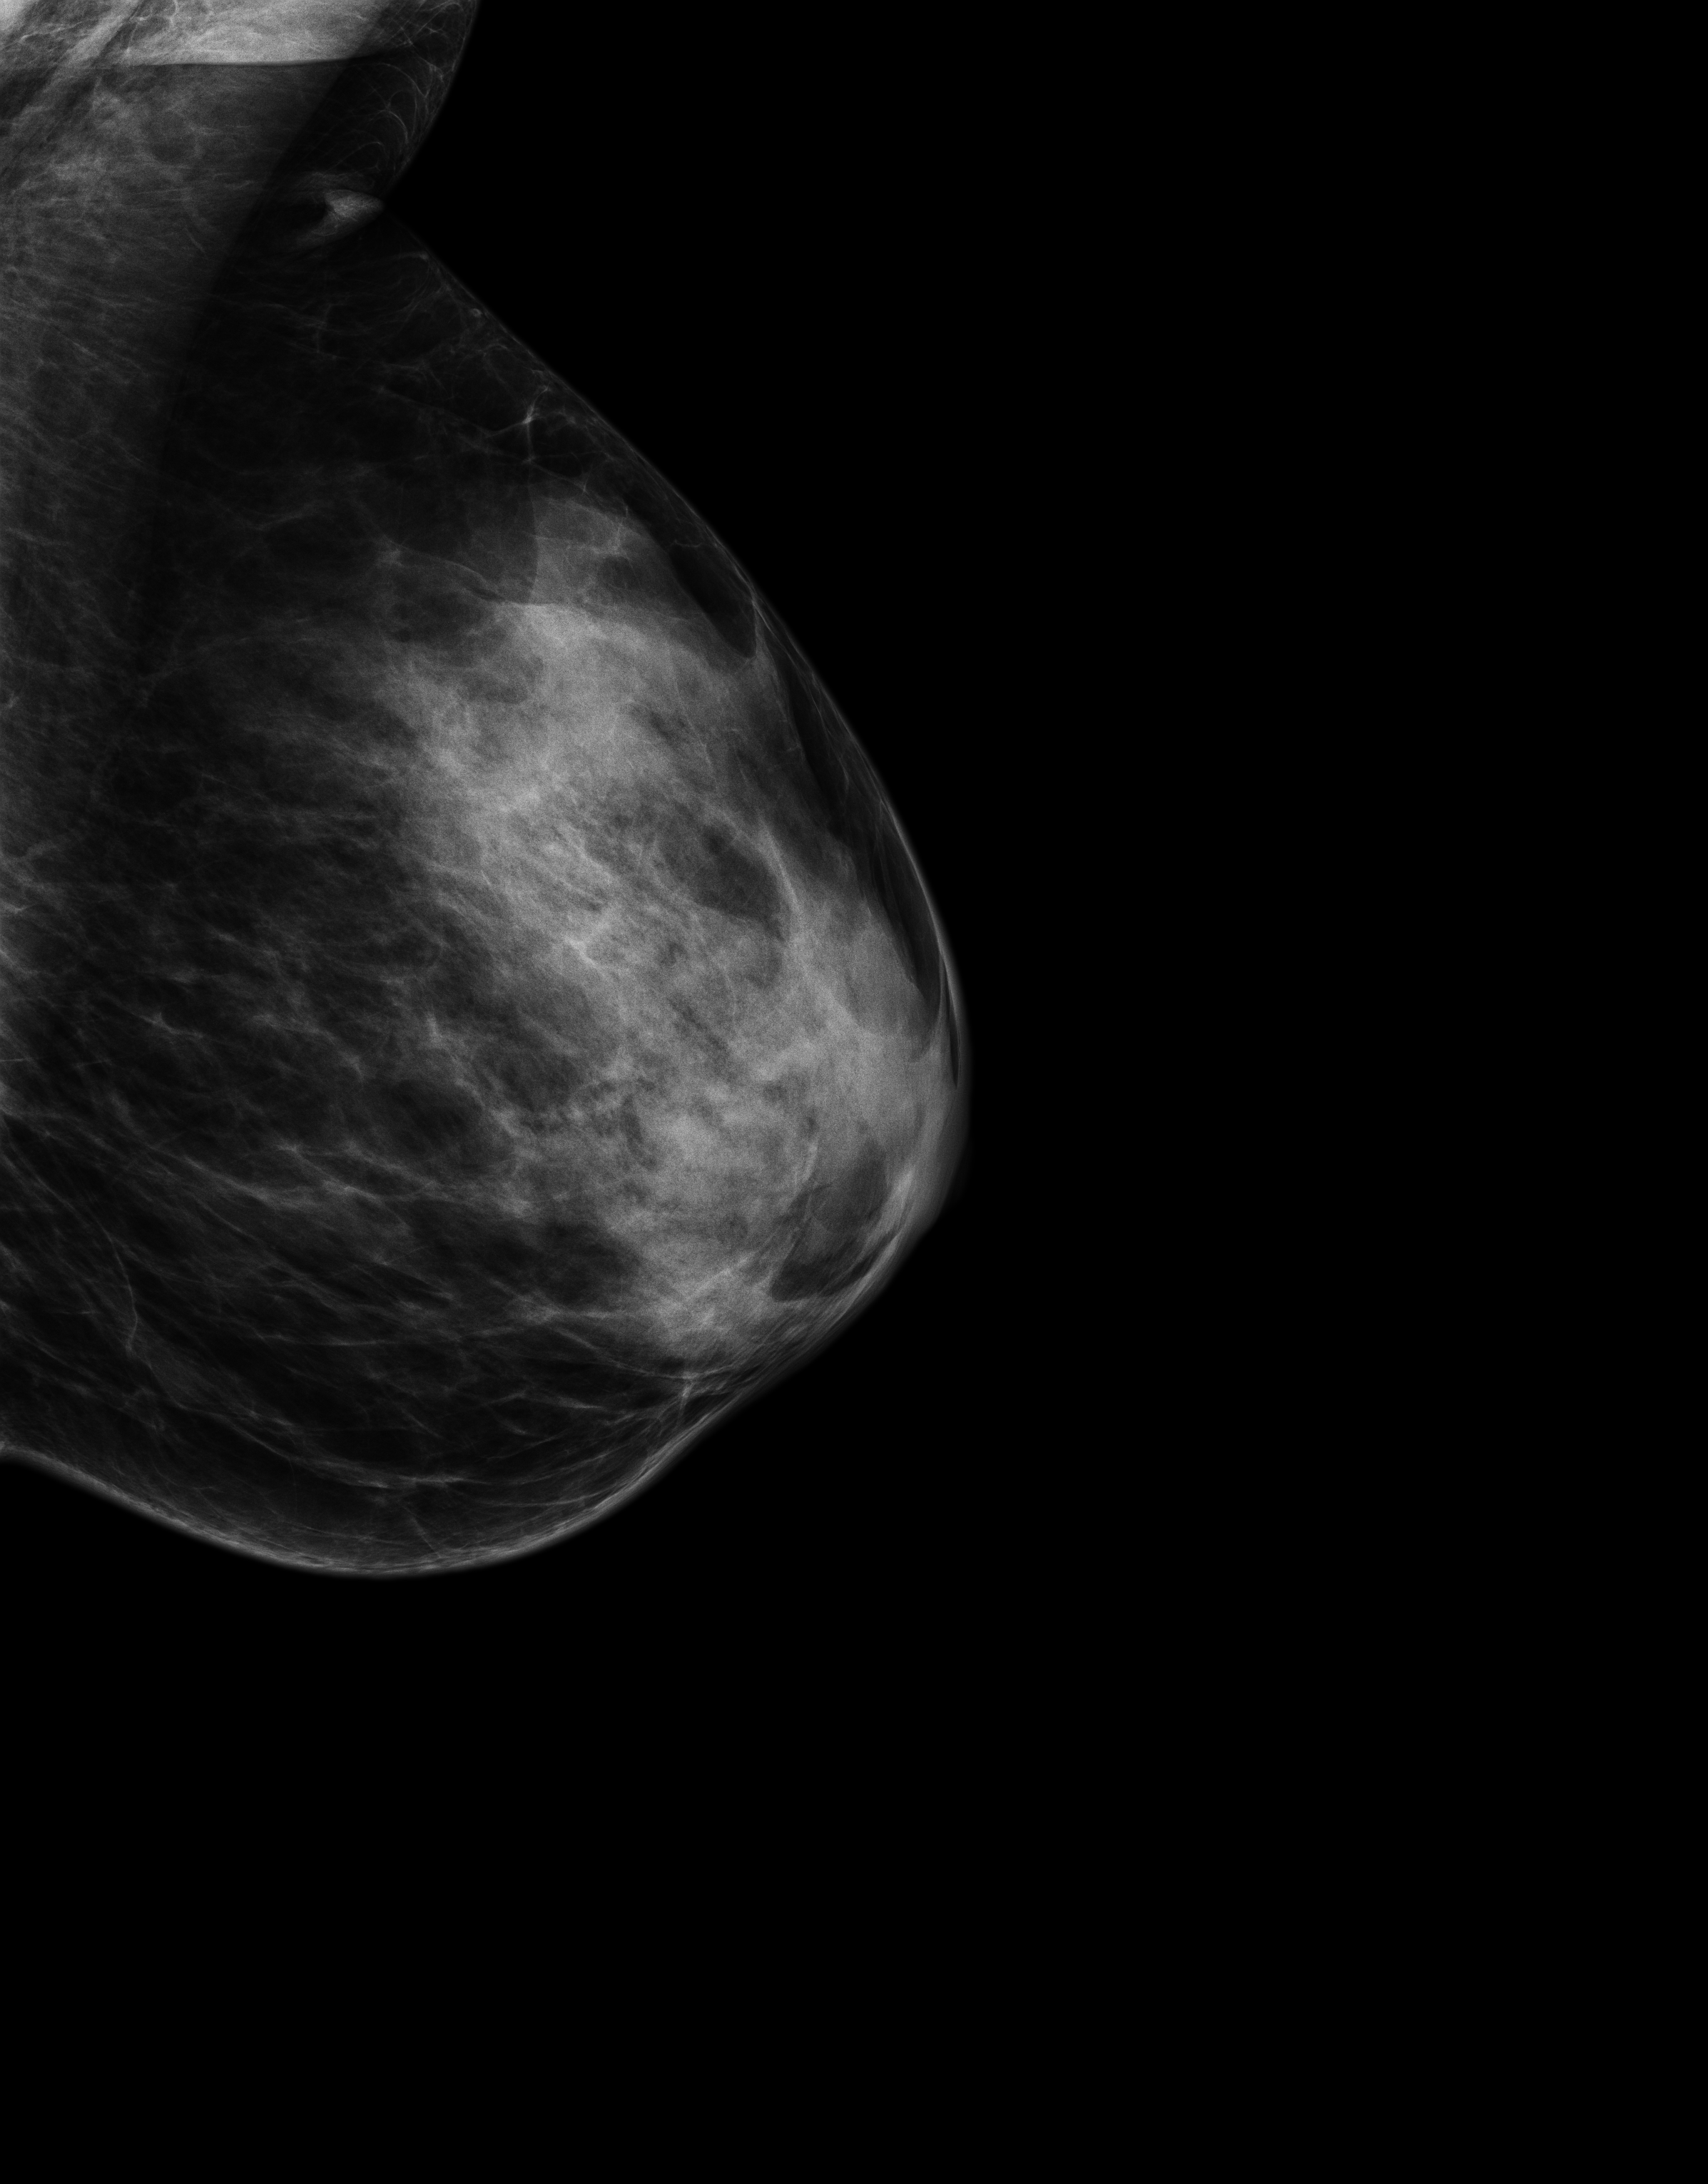
Digital mammogram (FFDM), left breast, MLO view, annual screening mammography examination. Patient: female, 48 years.
Breast density at the screening exam (both breasts): extremely dense (BI-RADS density category d). Final BI-RADS category for the screening round (tomosynthesis exam, both breasts): category 2. Recall: recalled for additional imaging after this screen.